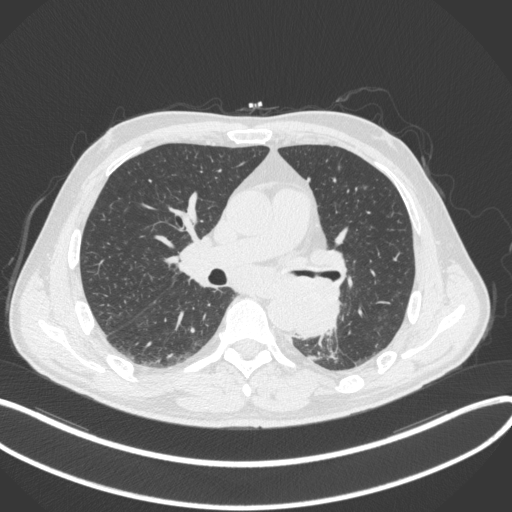
Chest CT, one axial slice. Position 190 of 328 along the scan axis. 120 kVp. Lung window (W 1500 / L -600 HU). 1 mm slice thickness. 512 × 512 image matrix, field of view 400 × 400 mm. Male patient, age 59 years. From the clinical record (not read from this slice): clinical TNM (as recorded): T2a N2 M0.
Outlined on this slice (rectangle marked by the reading radiologist):
- lung tumour (recorded histology: squamous cell carcinoma): bounding box [x1, y1, x2, y2] px = [291, 283, 345, 340]